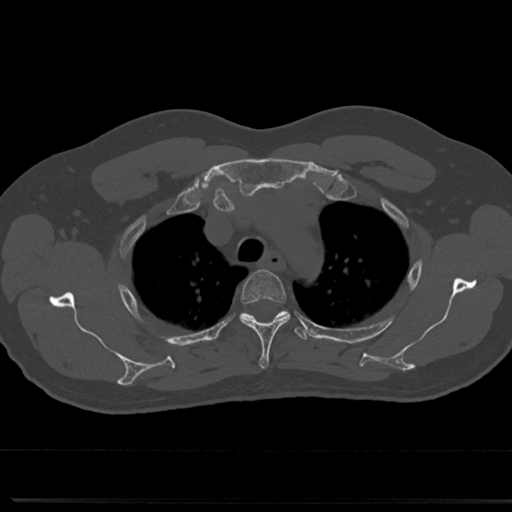
CT including the spine, one axial slice; slice 579 of 817 in the series (ordered by position); 120 kVp; bone window (W 1800 / L 400 HU); 512 × 512 image matrix, field of view 355 × 355 mm. Patient: male, 61 years. From the clinical record (not read from this slice): primary cancer: prostate.
Outlined on this slice (semi-automatic segmentation, software-assisted and operator-edited):
- T3 vertebra: bounding box <239,271,290,370> (left, top, right, bottom; pixels)
- T4 vertebra: <221,309,309,344>